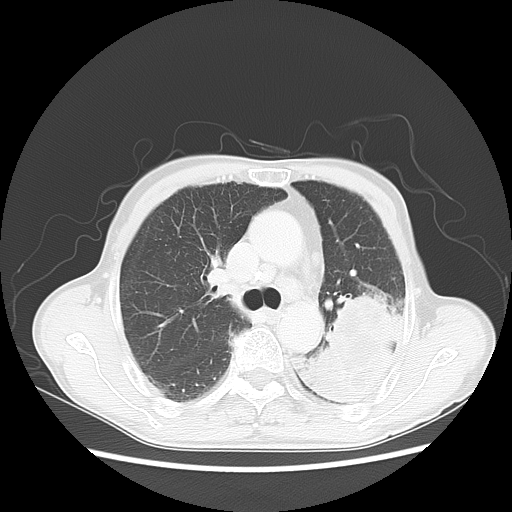
Chest CT, one axial slice; slice 35 of 51 in the series (ordered by position); 120 kVp; lung window (W 1500 / L -600 HU); 5 mm slice thickness; 512 × 512 image matrix, field of view 360 × 360 mm. Patient: male, 64 years. From the clinical record (not read from this slice): clinical TNM (as recorded): T4 N0 M0; histopathological grade: G2-3.
Outlined on this slice (rectangle marked by the reading radiologist):
- lung tumour (recorded histology: squamous cell carcinoma): bounding box (x1, y1, x2, y2) in pixels: (314, 289, 412, 406)